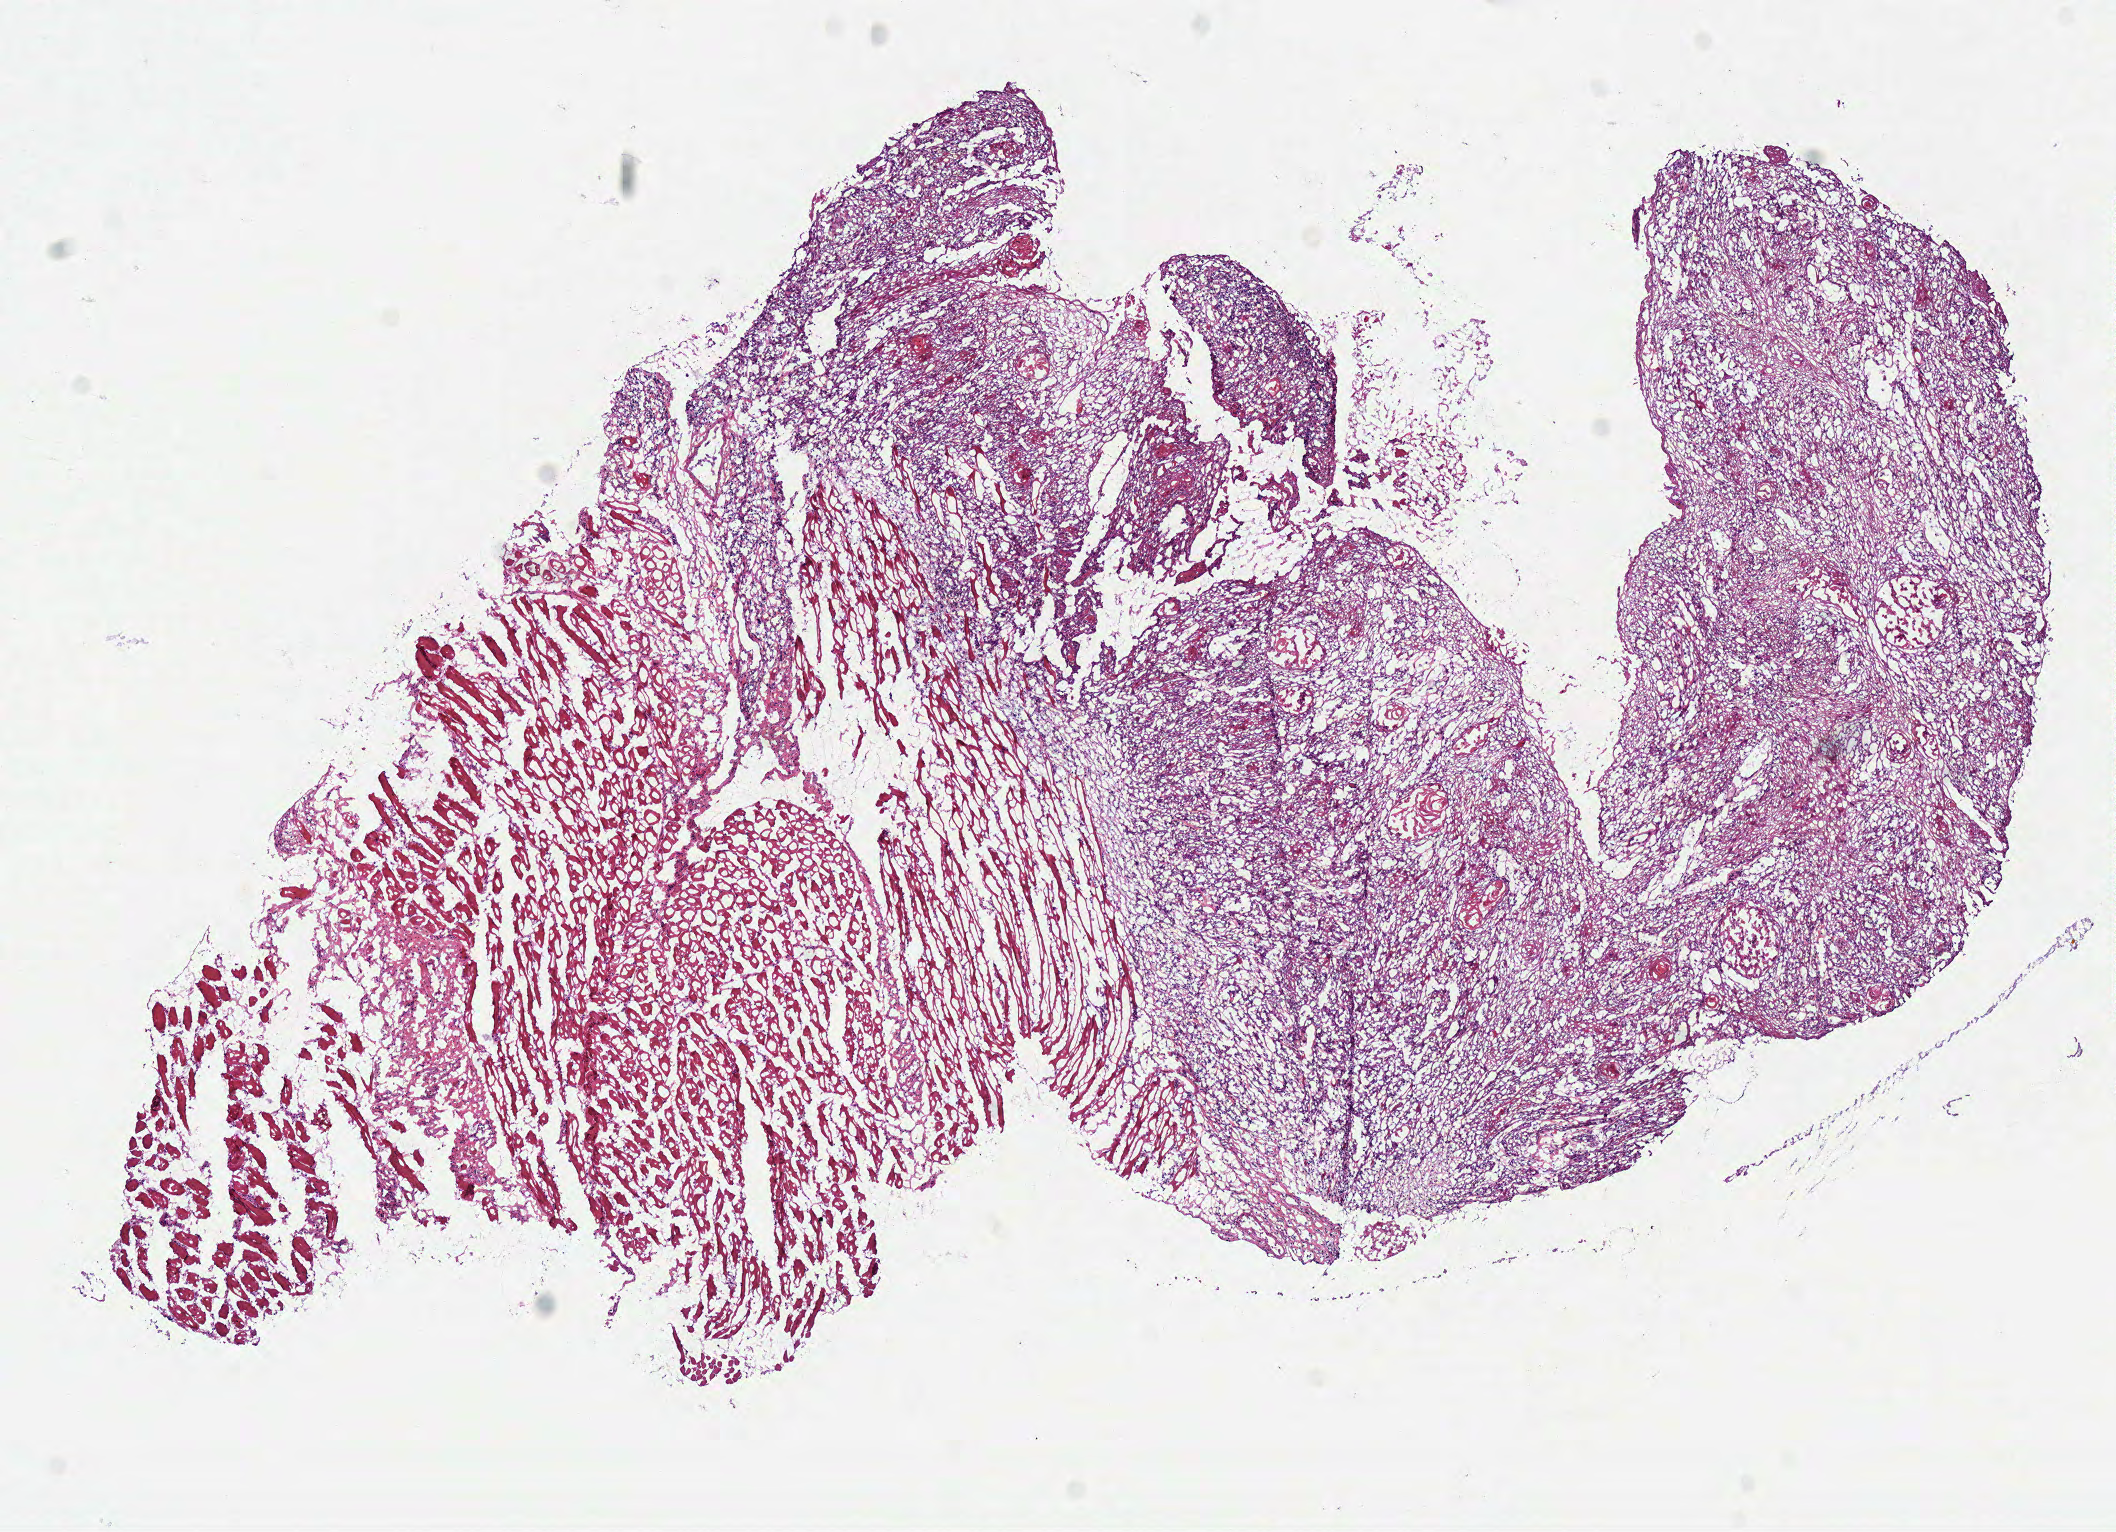
Whole-slide histology image, H&E-stained — whole scanned area (about 8.3 x 6.0 mm, from a 40x scan) shown as a low-resolution overview, frozen section, primary tumour sample from the head and neck. Female patient; age at initial diagnosis 52 years. Histologic grade: G2 (moderately differentiated). Slide review estimates, as recorded: tumour cells 60%, tumour nuclei 80%, normal cells 35%, stromal cells 5%, necrosis 0%.
- laterality: right
- diagnosis: Squamous cell carcinoma, NOS